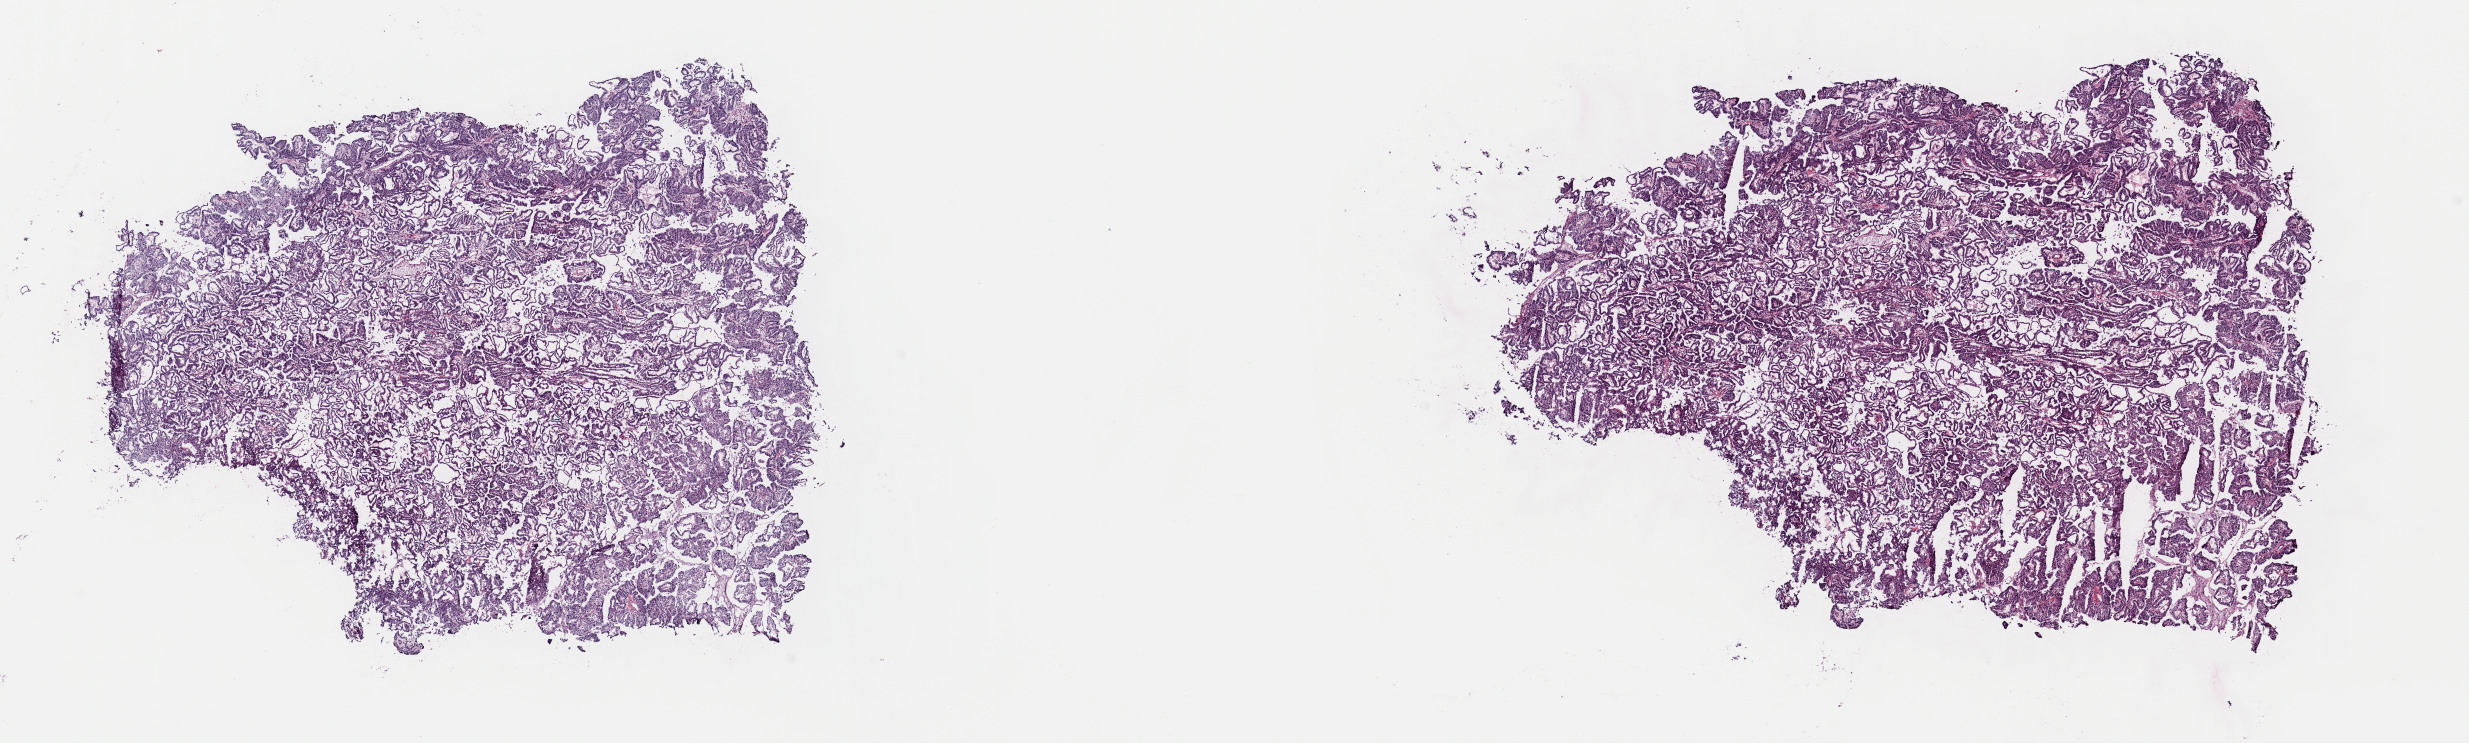
Digitized Hematoxylin and eosin (H&E) stained tissue section (whole slide) — a low-resolution overview of the entire scanned area, about 19.5 x 5.9 mm; frozen section from the top of the tissue portion; sample: primary tumour, kidney. Female patient; age at initial diagnosis 49 years. Pathologist review of this section (percent, as recorded): tumour cells 90%, tumour nuclei 90%, normal cells 0%, stromal cells 10%, necrosis 0%. Infiltration values recorded for this section: lymphocyte infiltration 0%, monocyte infiltration 0%, neutrophil infiltration 0%.
* laterality: left
* pathologic diagnosis: Papillary adenocarcinoma, NOS
* AJCC pathologic stage: I (7th edition)